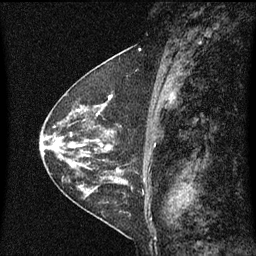
Breast MRI (dynamic contrast-enhanced), one sagittal slice; slice 31 of 60 in the series (ordered by position); dynamic contrast-enhanced series, image 2 of 3 at this slice position (ordered by acquisition); 1.5 T; TE 4.2 ms, TR 8 ms; 256 × 256 image matrix. Female patient, age 48 years.
Outlined on this slice (semi-automatically segmented with operator editing):
- analysis volume of interest (the breast-tissue region the enhancement analysis was run in; not a lesion): bounding box [x1, y1, x2, y2] px = [103, 74, 145, 139]
- tumour enhancement mask (voxels above the 70 % enhancement threshold inside the analysis volume of interest): [108, 94, 113, 139]